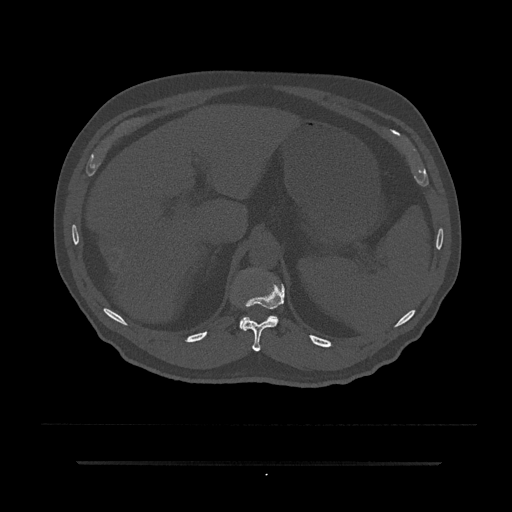
CT including the spine, one axial slice; slice 248 of 797 in the series (ordered by position); reconstruction kernel Br40s/3; 120 kVp; bone window (W 1800 / L 400 HU); 0.5 mm slice thickness; 512 × 512 image matrix. Patient: male, 59 years. Case-level facts recorded for this patient, not image findings: primary cancer: bile ducts; vertebrae with lytic lesions (as recorded): T10.
Annotated regions visible in this slice (semi-automatically segmented with operator editing):
- T11 vertebra: bounding box <241,282,285,352> (left, top, right, bottom; pixels)
- T12 vertebra: <240,316,279,328>